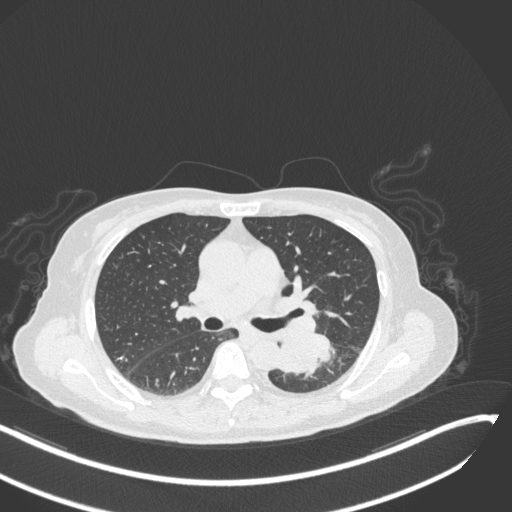
Chest CT, one axial slice; position 166 of 342 along the scan axis; lung window (W 1500 / L -600 HU); 1 mm slice thickness; 512 × 512 image matrix. Female patient, age 64 years. Case-level facts recorded for this patient, not image findings: clinical TNM (as recorded): T3 N1 M1.
Annotated regions visible in this slice (bounding box drawn by a radiologist):
- lung tumour (recorded histology: small cell carcinoma): bounding box (x1, y1, x2, y2) in pixels: (278, 333, 337, 380)